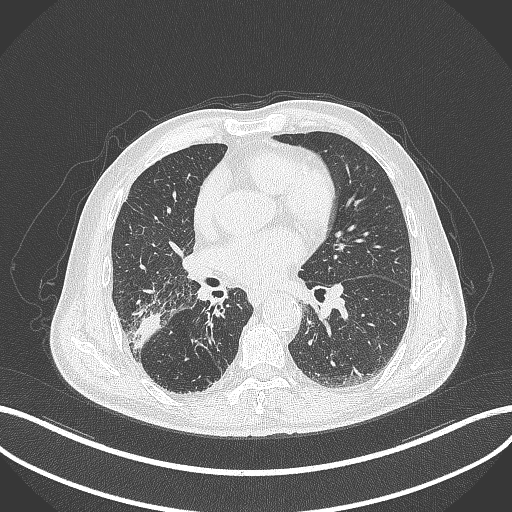
Chest CT, one axial slice; slice 203 of 429 in the series (ordered by position); reconstruction kernel B70f; lung window (W 1500 / L -600 HU); 512 × 512 image matrix, field of view 400 × 400 mm. Patient: male, 72 years. From the clinical record (not read from this slice): clinical TNM (as recorded): T3 N2 M0.
Outlined on this slice (bounding box drawn by a radiologist):
- lung tumour (recorded histology: adenocarcinoma): bounding box <126,310,165,353> (left, top, right, bottom; pixels)